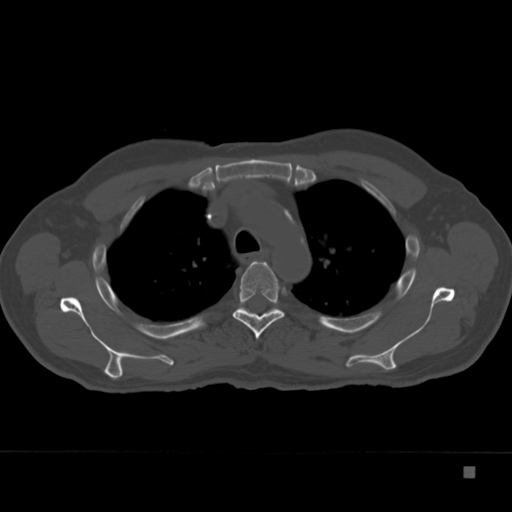
CT including the spine, one axial slice. Slice 271 of 332 in the series (ordered by position). 120 kVp. Bone window (W 1800 / L 400 HU). 512 × 512 image matrix, field of view 389 × 389 mm. Male patient, age 72 years. Case-level facts recorded for this patient, not image findings: primary cancer: skeletal.
Structures marked on this image (semi-automatically segmented with operator editing):
- T4 vertebra: box from (x=233, y=261) to (x=284, y=340) px
- T5 vertebra: (x=244, y=308)–(x=249, y=313)